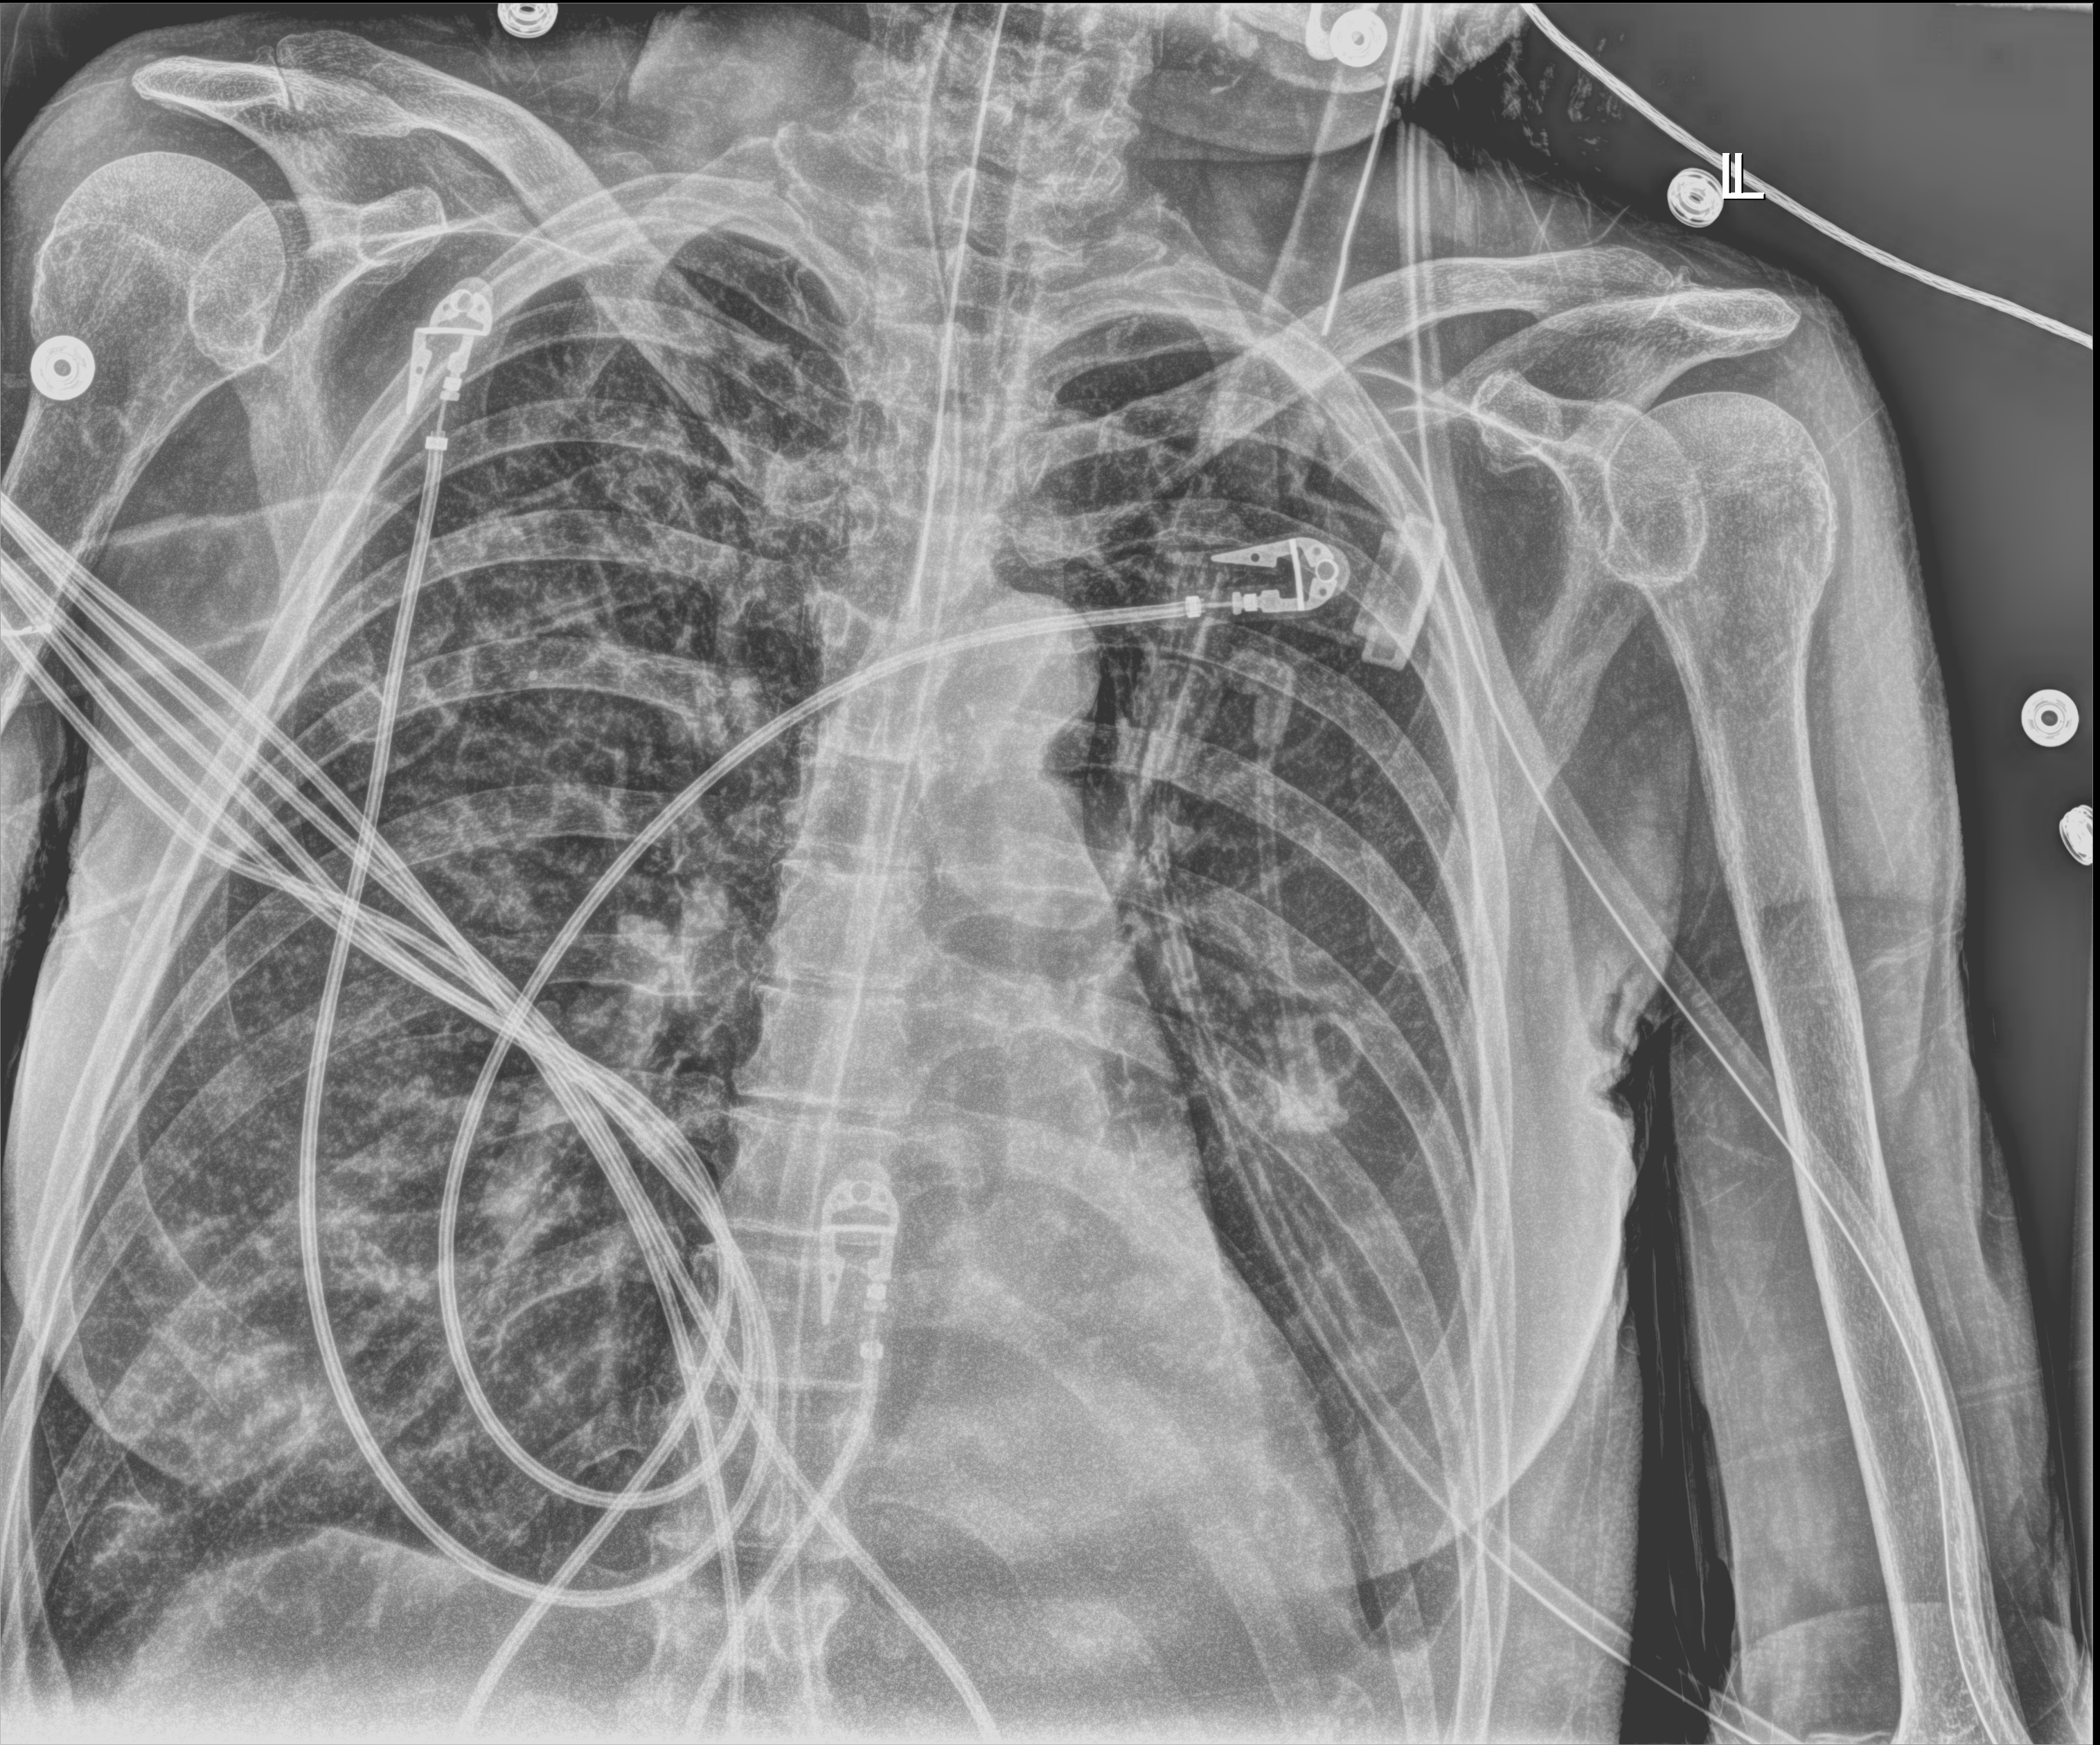
Chest X-ray (portable). Patient hospitalised with COVID-19; female, aged 60–74 years.
Admission-level facts for this patient (not findings on this image; timing relative to this image not recorded):
- mechanically ventilated during this hospital stay: yes